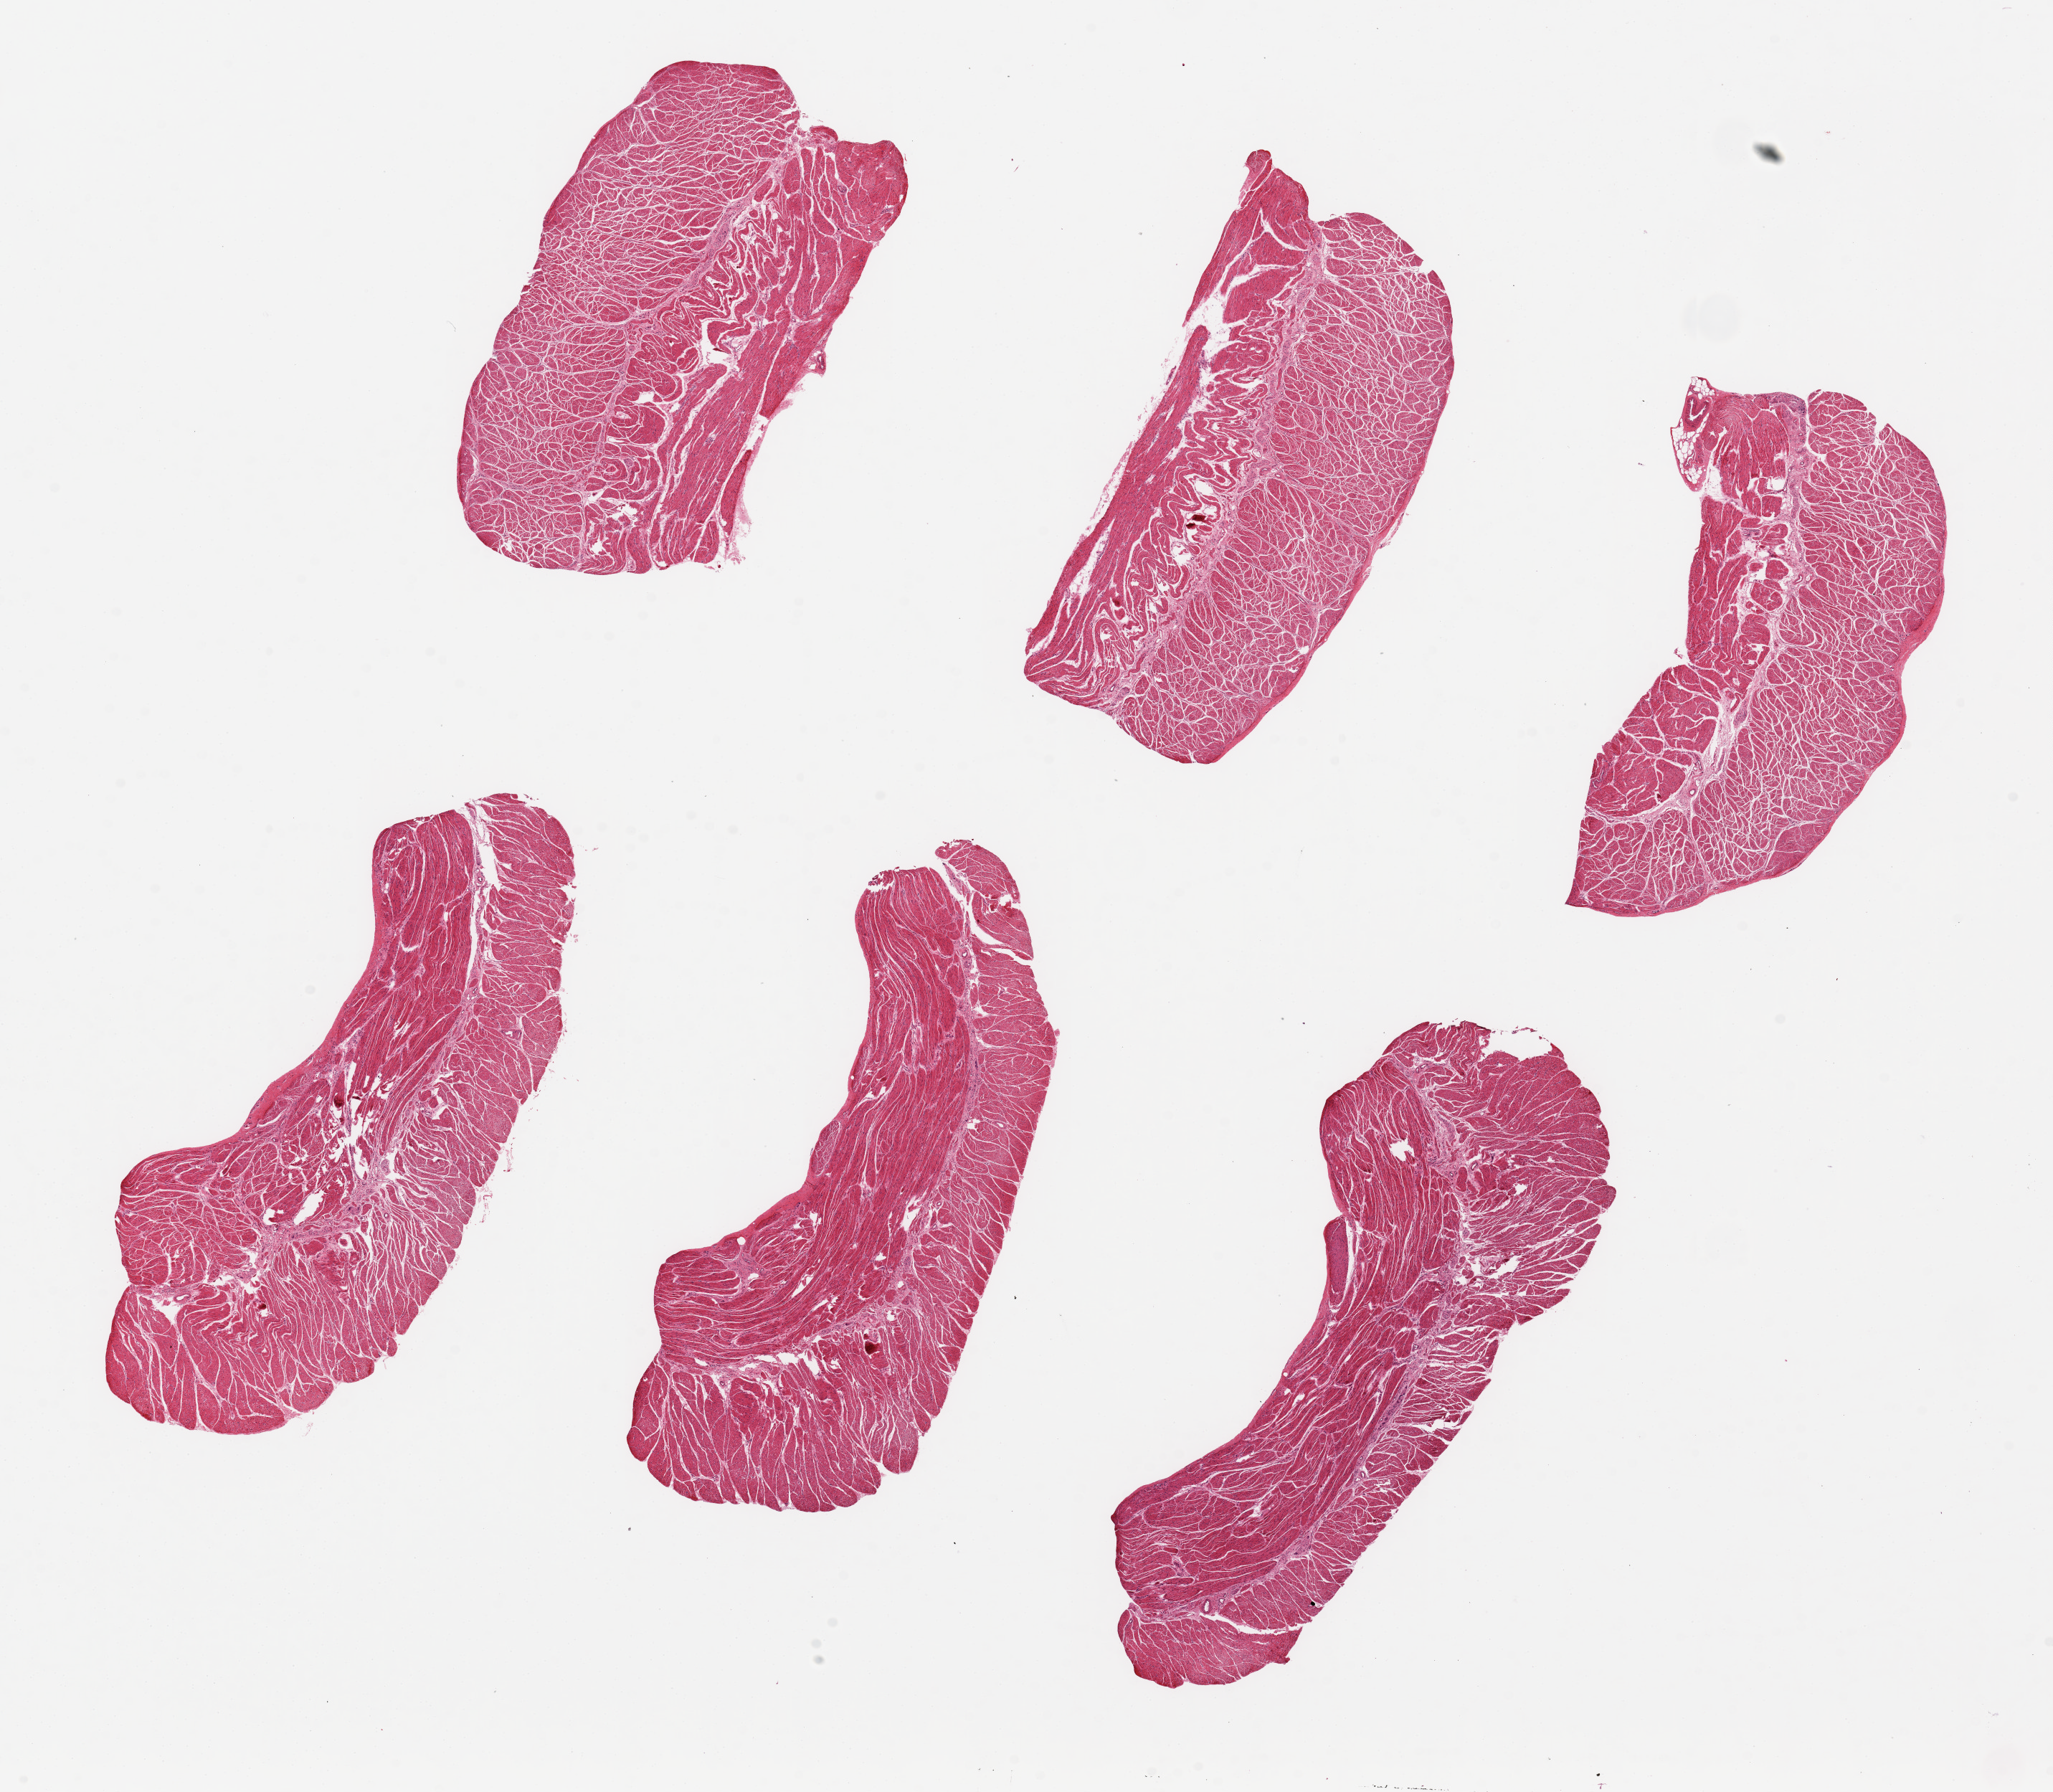
Whole-slide image, hematoxylin and eosin (H&E) stain — low-resolution overview of the scanned area, about 22.6 x 19.8 mm (slide scanned at 20x). PAXgene-fixed, paraffin-embedded tissue. Sampled site (target tissue): esophageal muscle. Donor tissue sample. Donor sex: male.
• reviewer comment on this tissue sample: 6 pieces ~6x3mm